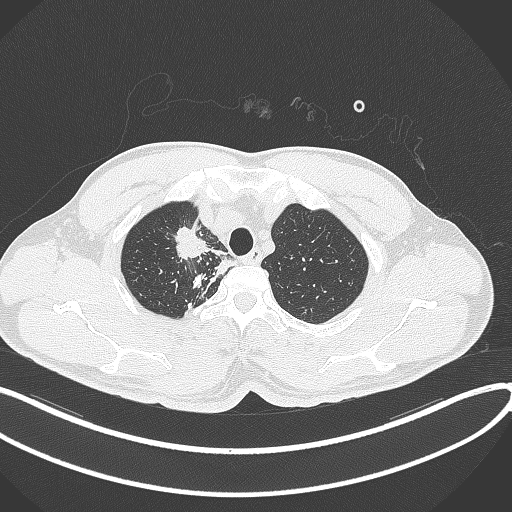
Chest CT, one axial slice; slice 324 of 391 in the series (ordered by position); 120 kVp; lung window (W 1500 / L -600 HU); 1 mm slice thickness; 512 × 512 image matrix, field of view 400 × 400 mm. Patient: male, 48 years. Case-level facts recorded for this patient, not image findings: clinical TNM (as recorded): T1c N1 M1.
Annotated regions visible in this slice (bounding box drawn by a radiologist):
- lung tumour (recorded histology: adenocarcinoma): bounding box [x1, y1, x2, y2] px = [171, 225, 215, 261]